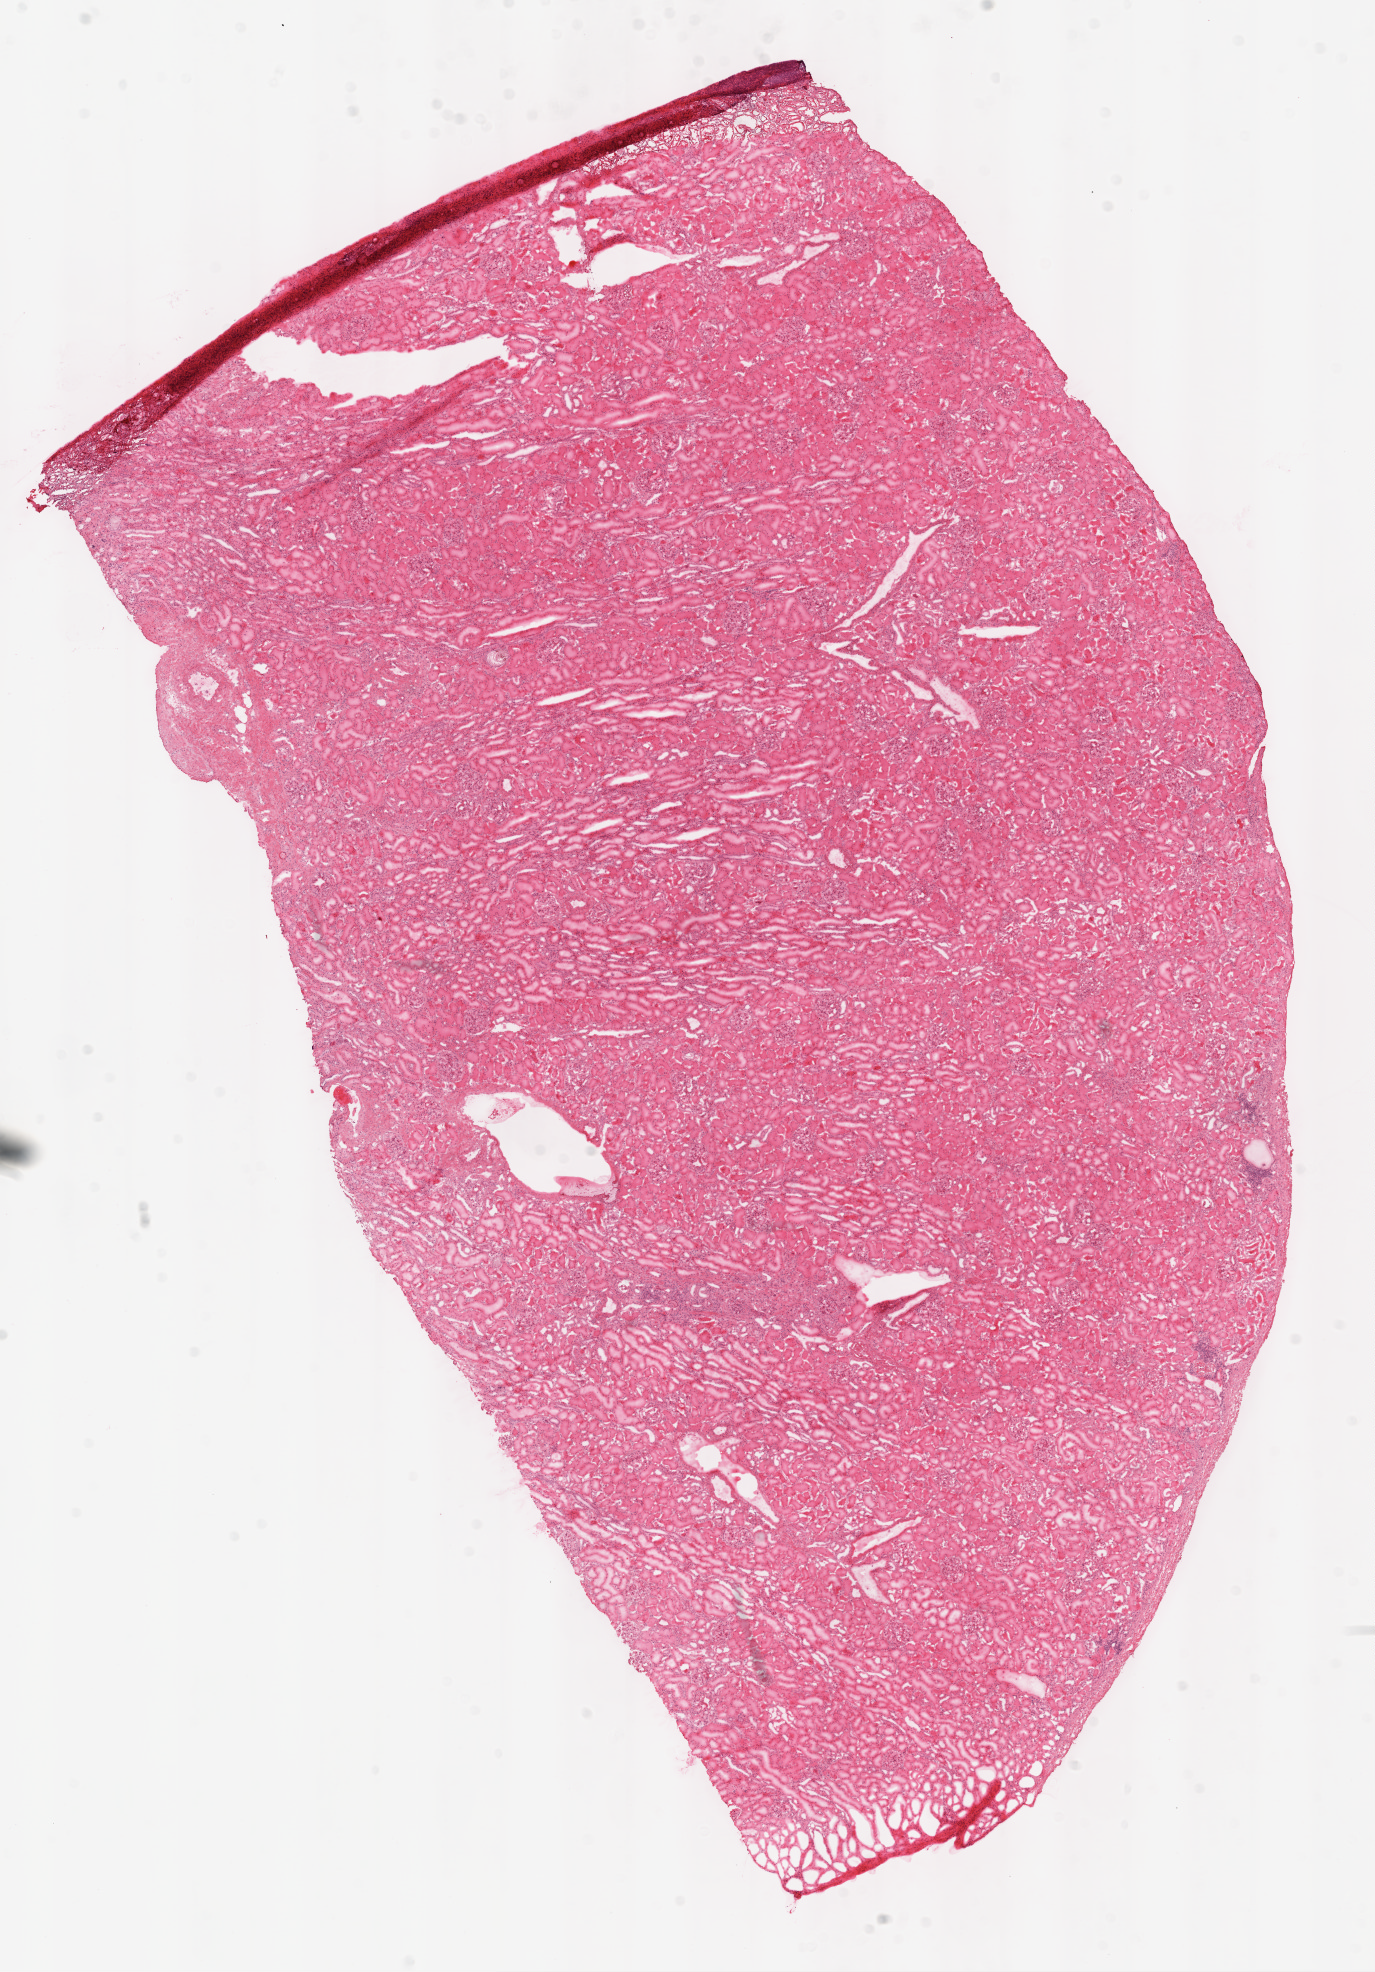
Digitized Hematoxylin and eosin (H&E) stained tissue section (whole slide), a low-resolution overview of the entire scanned area, about 11.0 x 15.8 mm, frozen section, sample: solid tissue normal (non-tumour tissue), kidney. Female, age 60 years at initial diagnosis.
* this section: solid tissue normal (non-tumour) sample from the same patient
* patient diagnosis: Clear cell adenocarcinoma, NOS